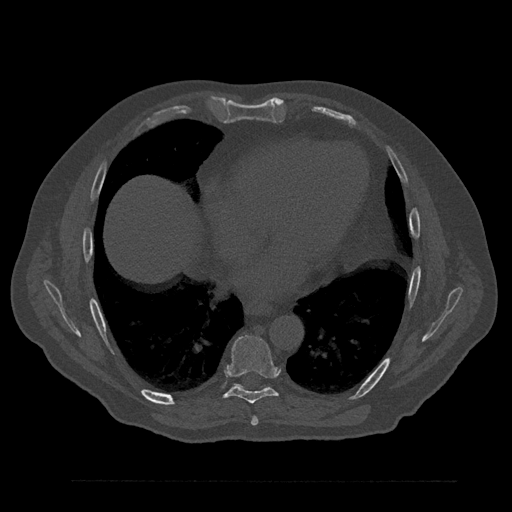
CT including the spine, one axial slice; slice 450 of 797 in the series (ordered by position); reconstruction kernel Br40s/3; 120 kVp; bone window (W 1800 / L 400 HU); 0.5 mm slice thickness; 512 × 512 image matrix, field of view 430 × 430 mm. Patient: male, 61 years. From the clinical record (not read from this slice): primary cancer: prostate.
Outlined on this slice (semi-automatic segmentation, software-assisted and operator-edited):
- T7 vertebra: bounding box (x1, y1, x2, y2) in pixels: (251, 416, 258, 426)
- T8 vertebra: (215, 335, 278, 406)